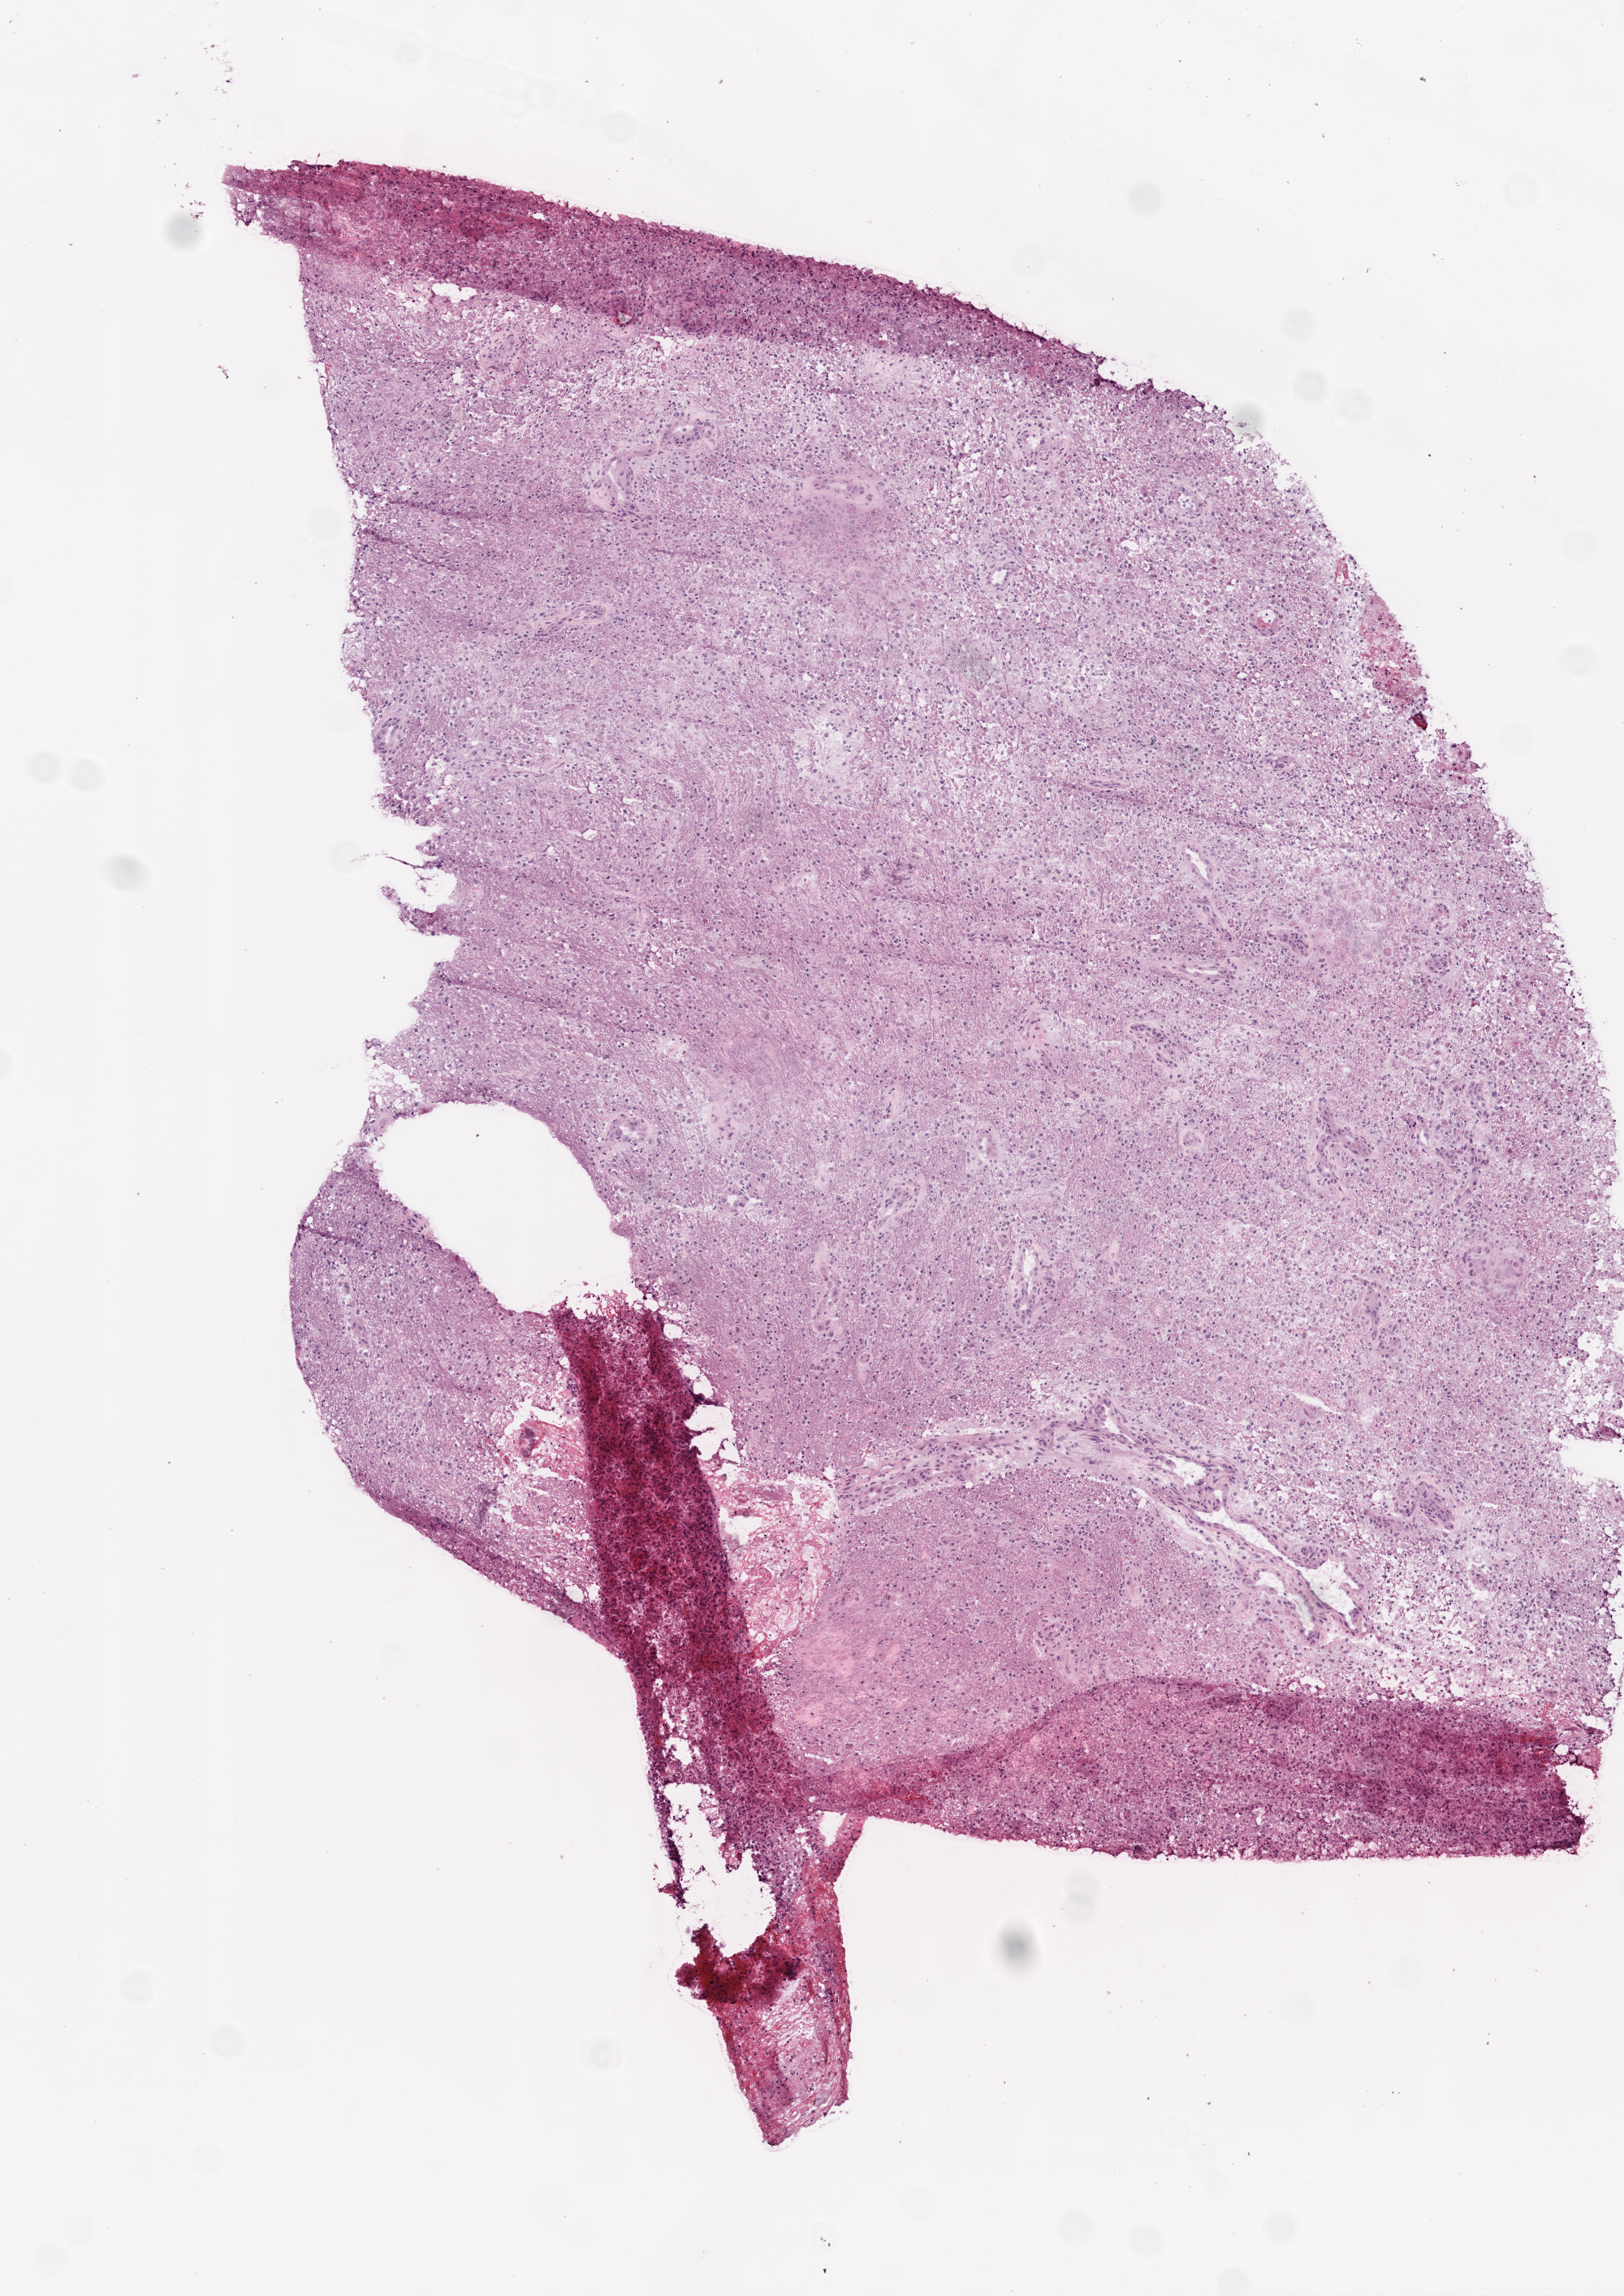
Hematoxylin and eosin (H&E) stained whole-slide image, shown as a low-resolution overview of the whole scanned area (about 4.0 x 5.7 mm); frozen section from the top of the tissue portion; primary tumour sample from the brain. Female, age 58 years at initial diagnosis. Composition of this section per pathologist review: tumour cells 60%, tumour nuclei 60%, normal cells 35%, stromal cells 5%, necrosis 0%.
- pathologic diagnosis: Glioblastoma